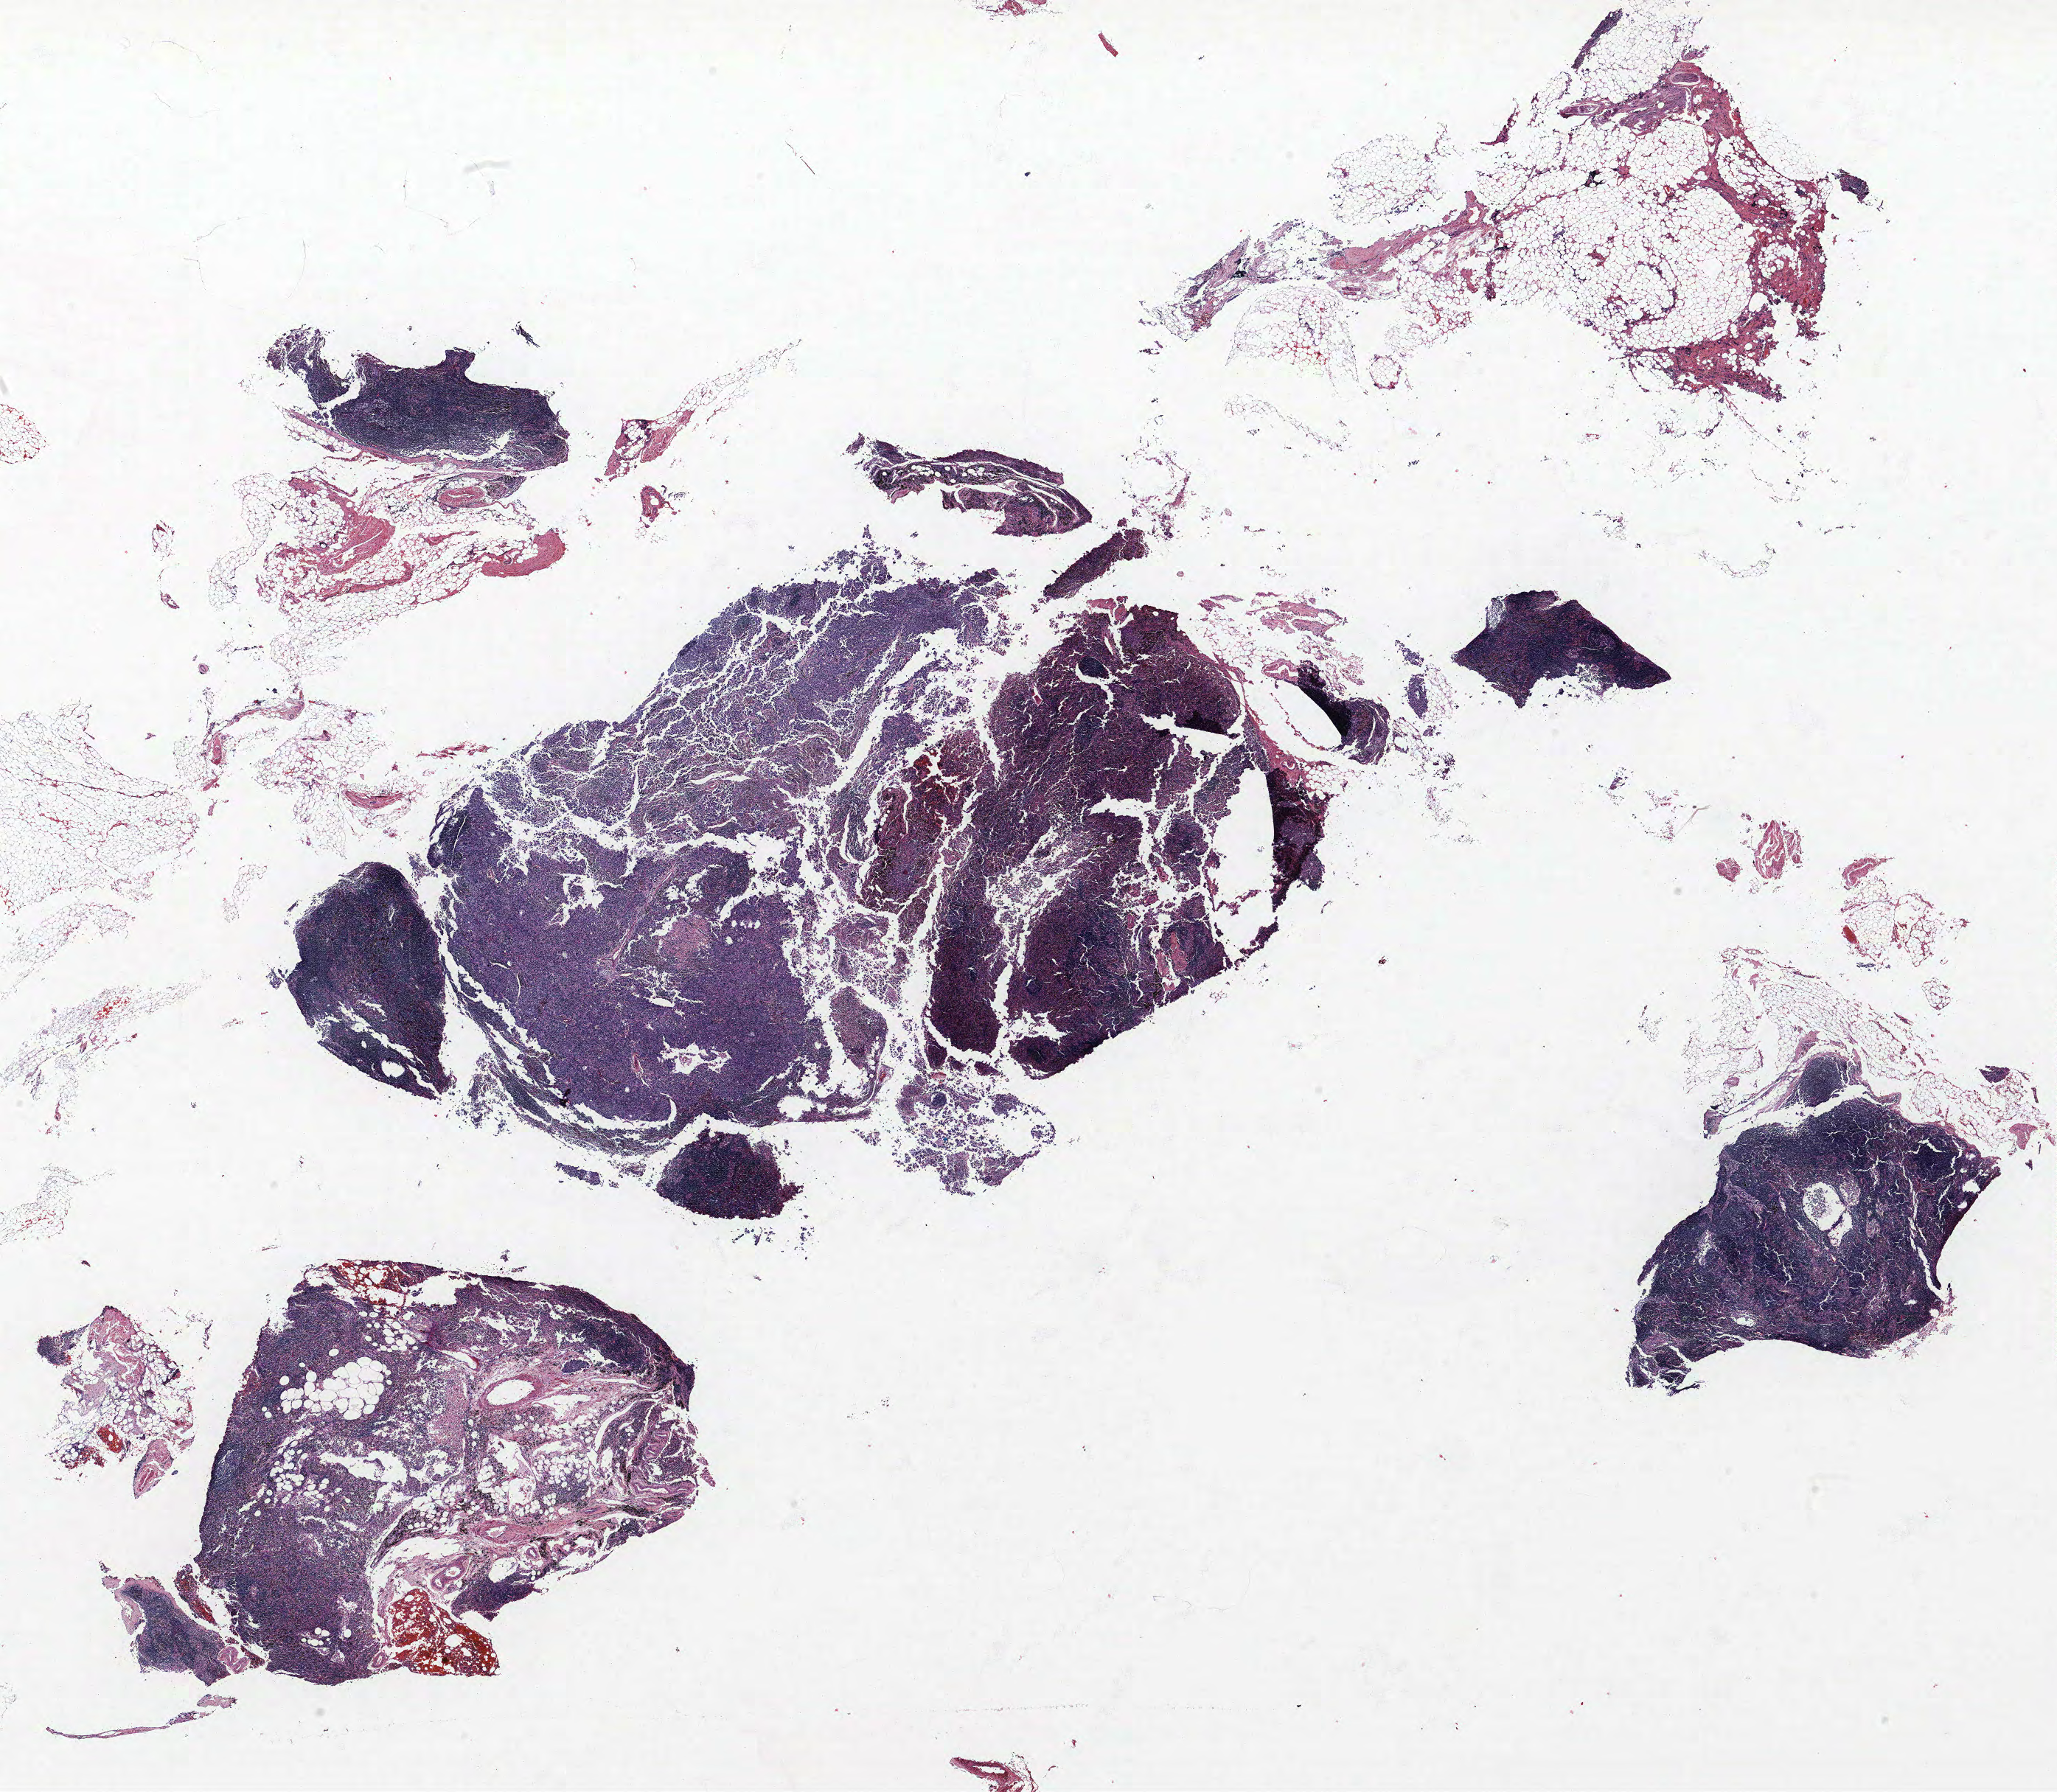
Whole-slide histology image, H&E-stained, a low-resolution overview of the entire scanned area, about 22.3 x 19.5 mm (from a 40x scan). Formalin-fixed paraffin-embedded (FFPE) section. Lung. Female, age 62 at enrolment. Former smoker at enrolment. Grade: cannot be assessed (GX).
ICD-O-3 topography: upper lobe of lung (C34.1). Participant's lung-cancer diagnosis: Squamous cell carcinoma, NOS. Primary tumour location (clinical record): right upper lobe. Tumour size (pathology): 27 mm. Stage (AJCC 6th edition): IIIA.